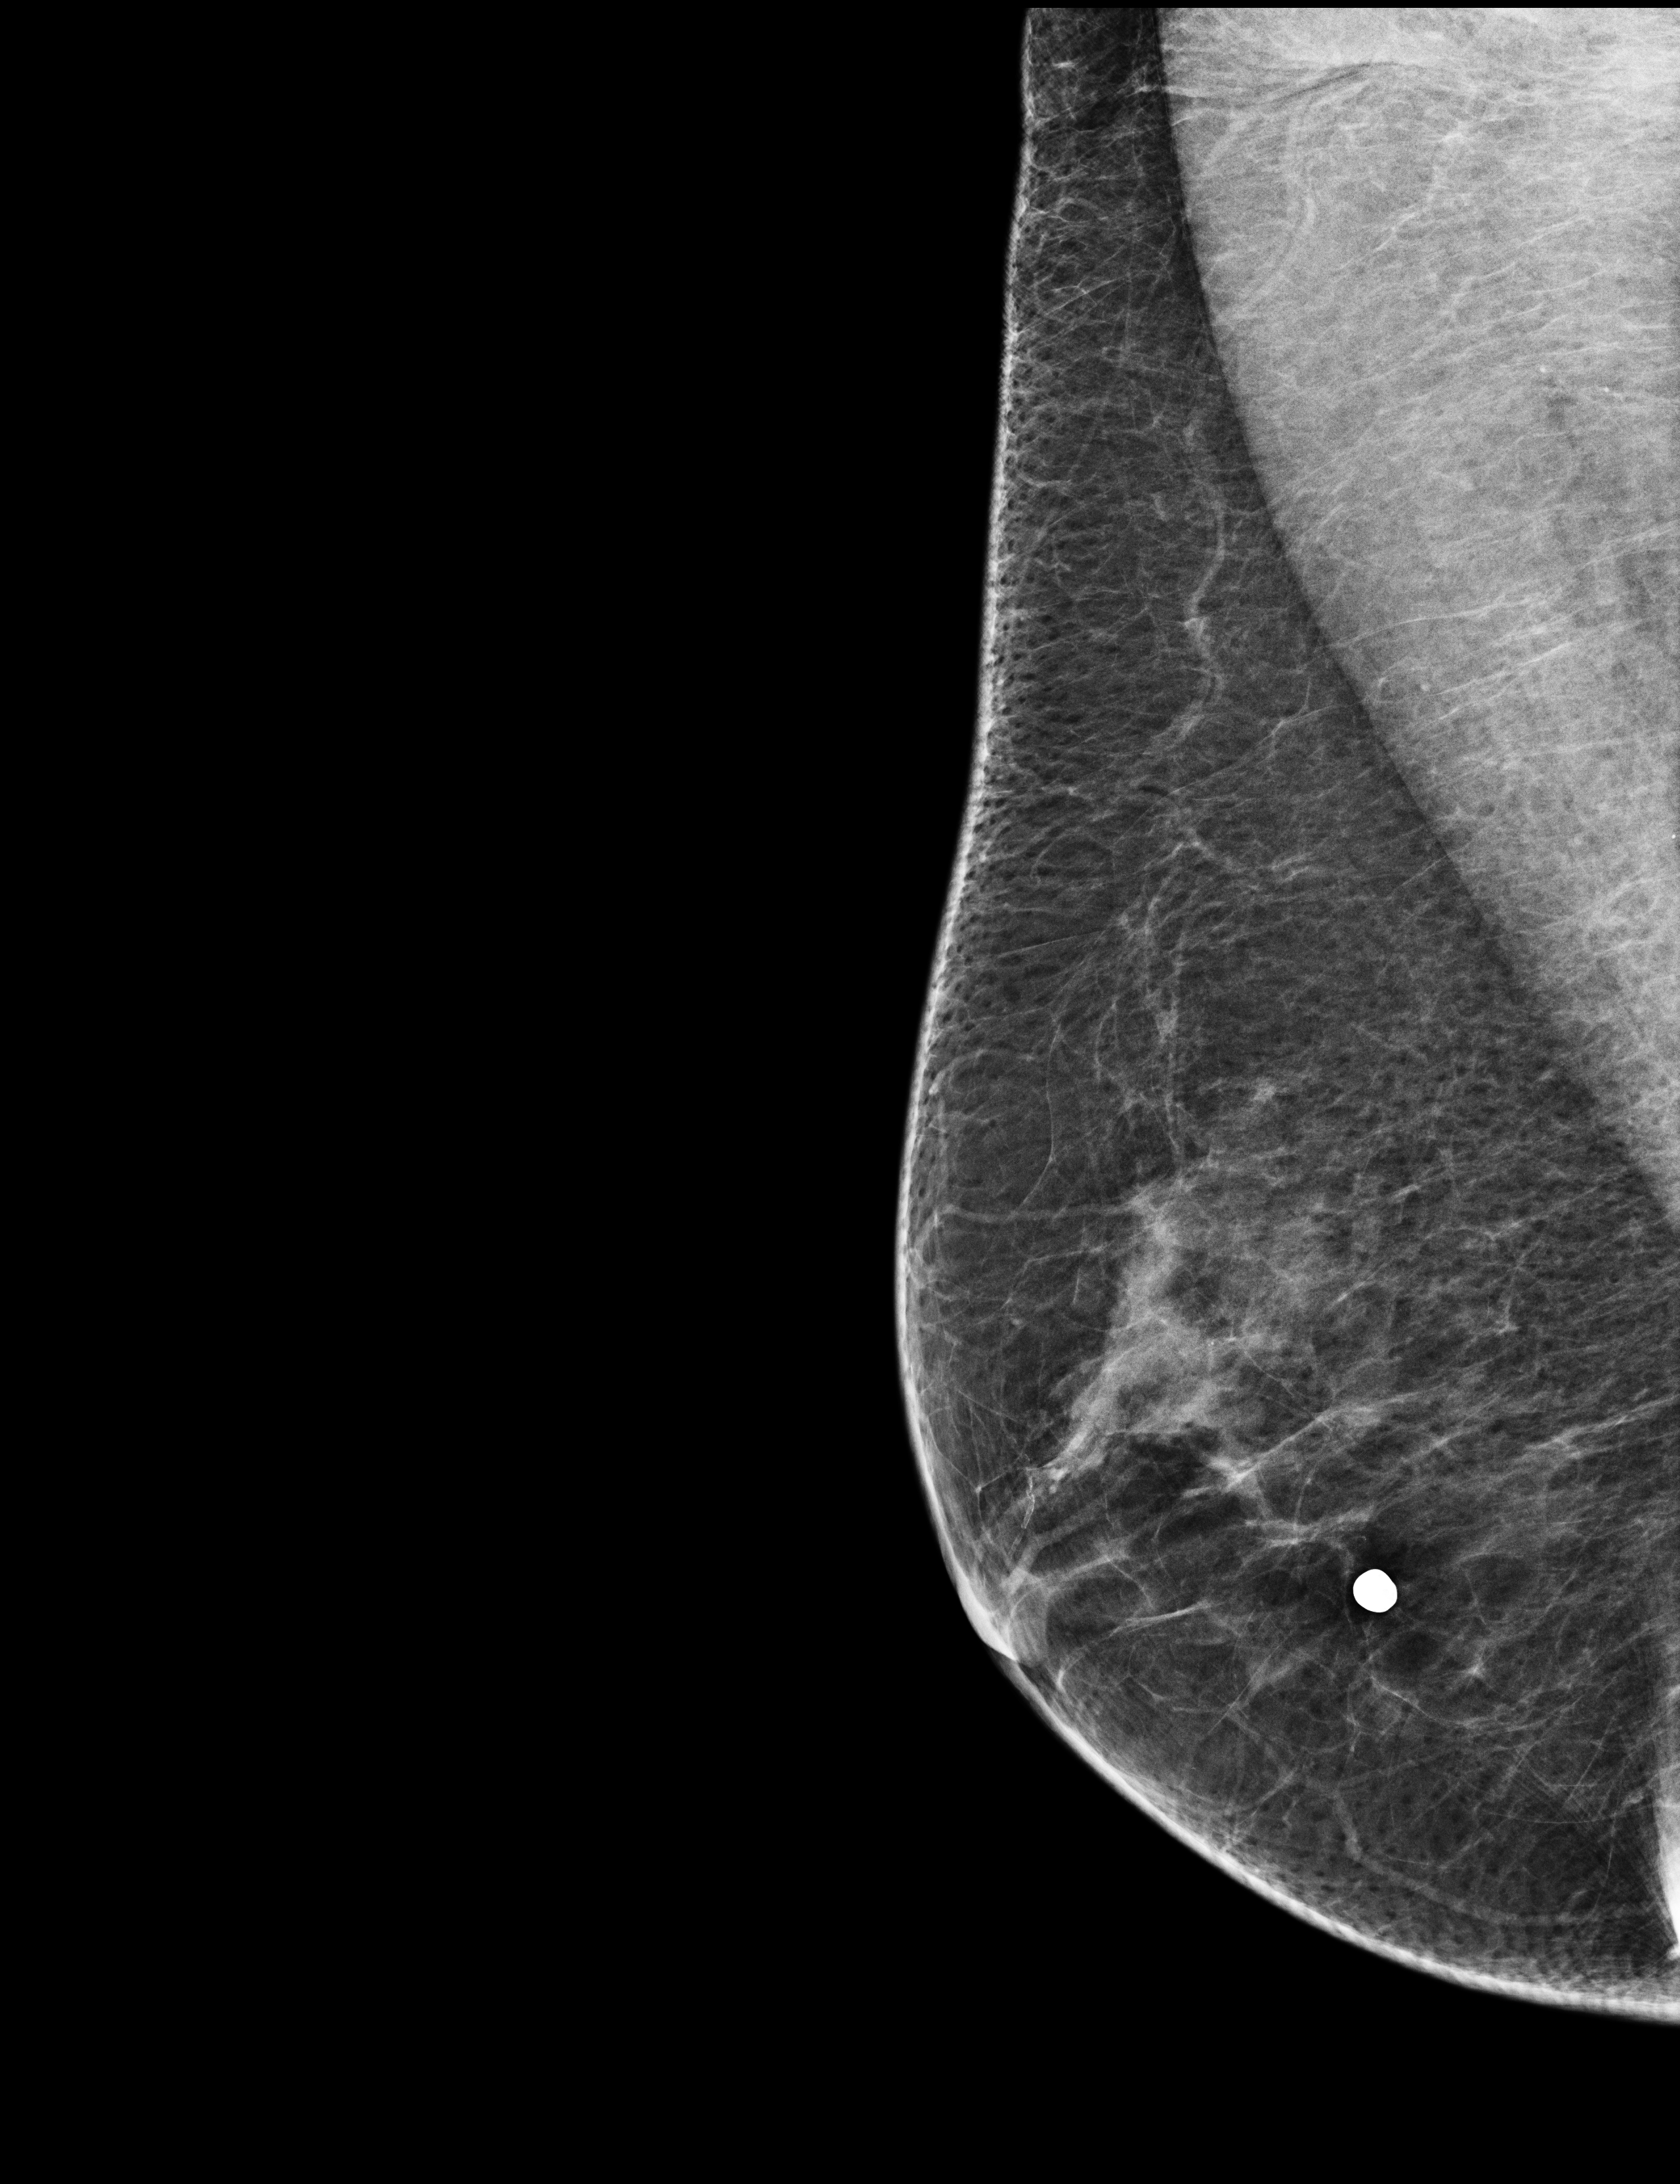
Annual screening mammography examination. Patient: female, 75 years.
Image type: full-field digital mammogram. Breast: right. Projection: mediolateral oblique (MLO) view.